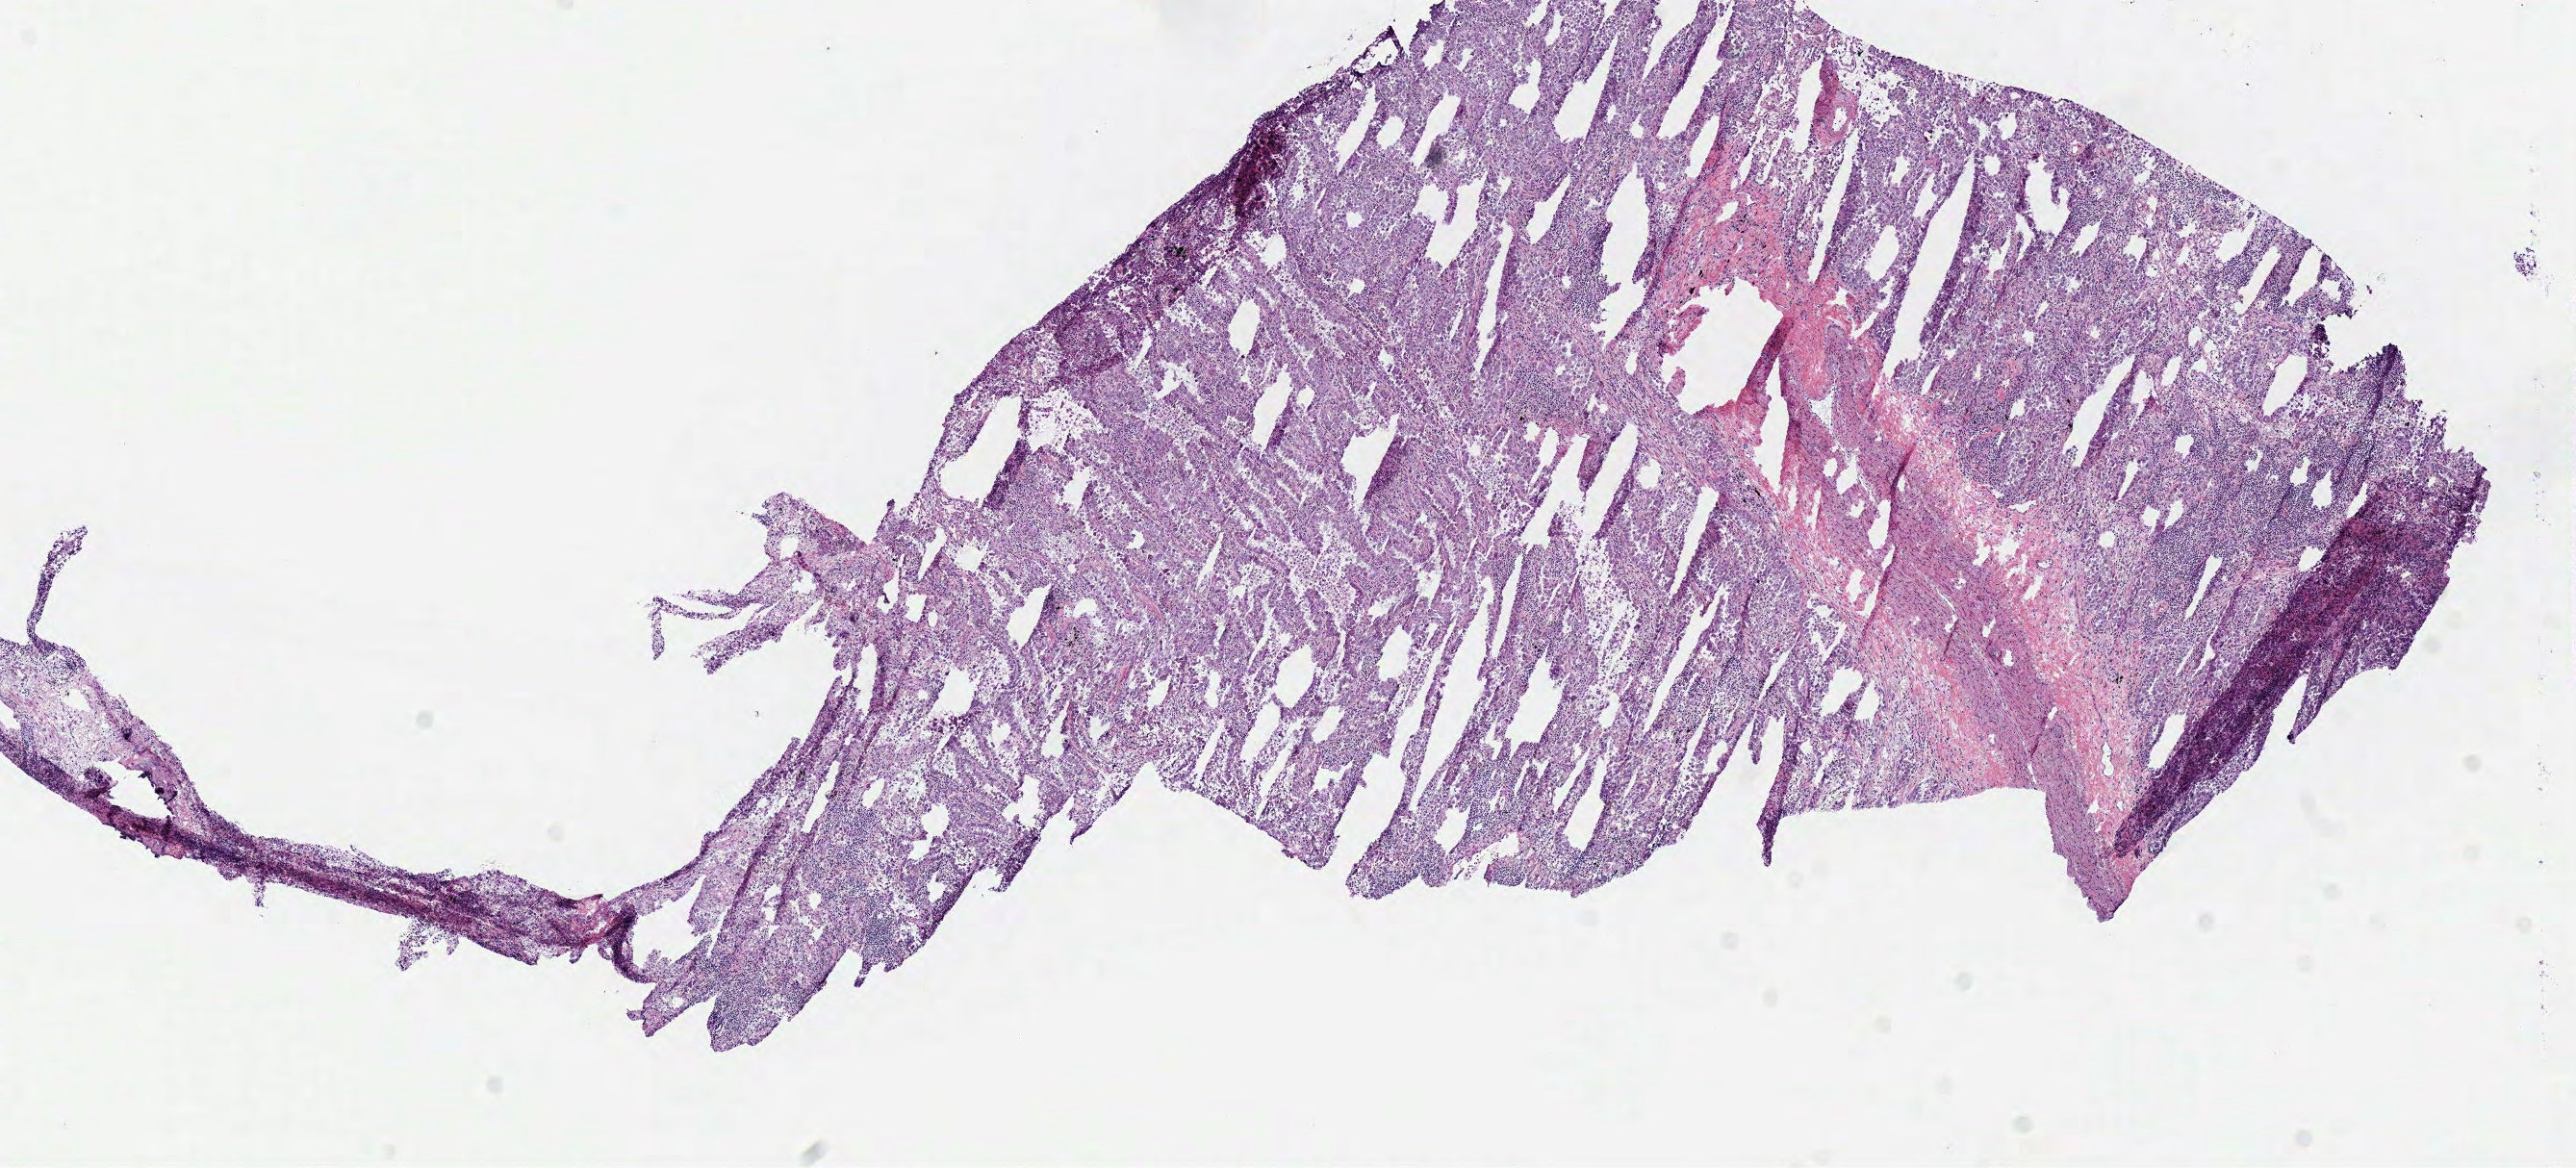
Digitized H&E-stained tissue section (whole slide) — low-resolution overview of the scanned area, about 10.5 x 4.8 mm; frozen section; sample: primary tumour, lung. Female patient; age at initial diagnosis 81 years. Composition of this section per pathologist review: tumour cells 70%, tumour nuclei 75%, normal cells 0%, stromal cells 10%, necrosis 20%.
TNM: T1 N0 M0. AJCC pathologic stage: IA (7th edition). Histologic diagnosis: Adenocarcinoma, NOS (lower lobe, lung). Laterality: right.